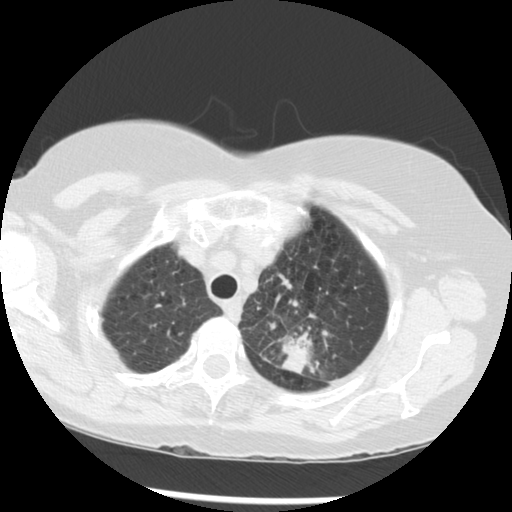
Chest CT (low-dose screening protocol), one axial image; third annual screen; lung window (W 1500 / L -600 HU); 2.5 mm slice thickness; standard (soft-tissue) reconstruction kernel (STANDARD); slice 238 of 283 in the series. Female participant, aged 70 years at enrolment.
Lesion marked by an expert reader, bounding box (x1, y1, x2, y2) in pixels: (250, 287, 348, 375). Reader record for this screening exam (exam-level; its link to the box is not recorded): non-calcified nodule or mass ≥4 mm, left upper lobe, 32 × 26 mm, spiculated (stellate) margins, soft tissue attenuation, pre-existing on the prior screen: yes; interval growth: yes. Official screen result: positive, other. Later outcome: lung cancer diagnosed 24 days after this screen — neoplasm, malignant, left upper lobe, stage IIIB (AJCC 6th edition), 40 mm at pathology.